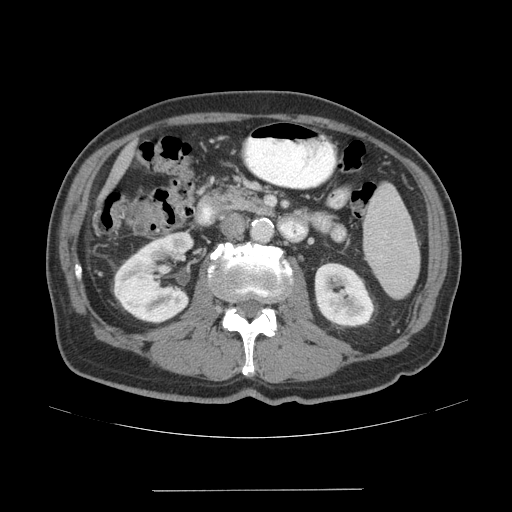
Contrast-enhanced abdominal CT (liver protocol), one axial slice; reconstruction kernel STANDARD; 140 kVp; soft-tissue window (W 400 / L 40 HU); 2.5 mm slice thickness; 512 × 512 image matrix, field of view 400 × 400 mm. From the clinical record (not read from this slice): diagnosis: hepatocellular carcinoma (patient treated with transarterial chemoembolisation; whether this scan precedes or follows treatment is not stated here); TNM stage (as recorded): Stage-IVA; Child-Pugh class: A; tumour differentiation: well differentiated; tumour nodularity: uninodular.
Structures marked on this image (semi-automatically segmented with operator editing):
- liver parenchyma outside the tumour (the mass and vessels are separate outlines, so this box may not span the whole liver): box from (x=96, y=142) to (x=134, y=213) px